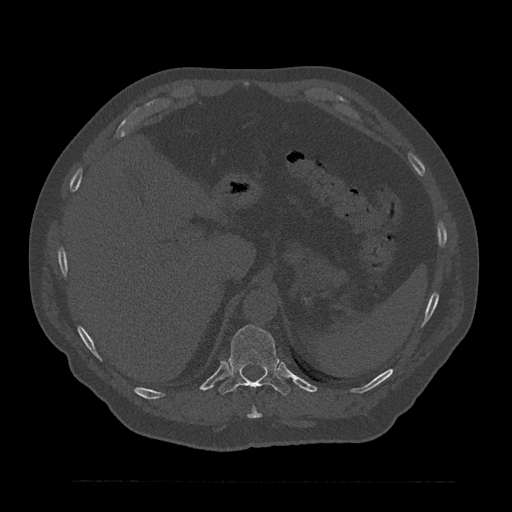
CT including the spine, one axial slice; slice 304 of 797 in the series (ordered by position); 120 kVp; bone window (W 1800 / L 400 HU); 0.5 mm slice thickness; 512 × 512 image matrix, field of view 430 × 430 mm. Male patient, age 61 years. From the clinical record (not read from this slice): primary cancer: prostate.
Outlined on this slice (semi-automatically segmented with operator editing):
- T10 vertebra: bounding box <247,406,262,419> (left, top, right, bottom; pixels)
- T11 vertebra: <219,325,290,396>